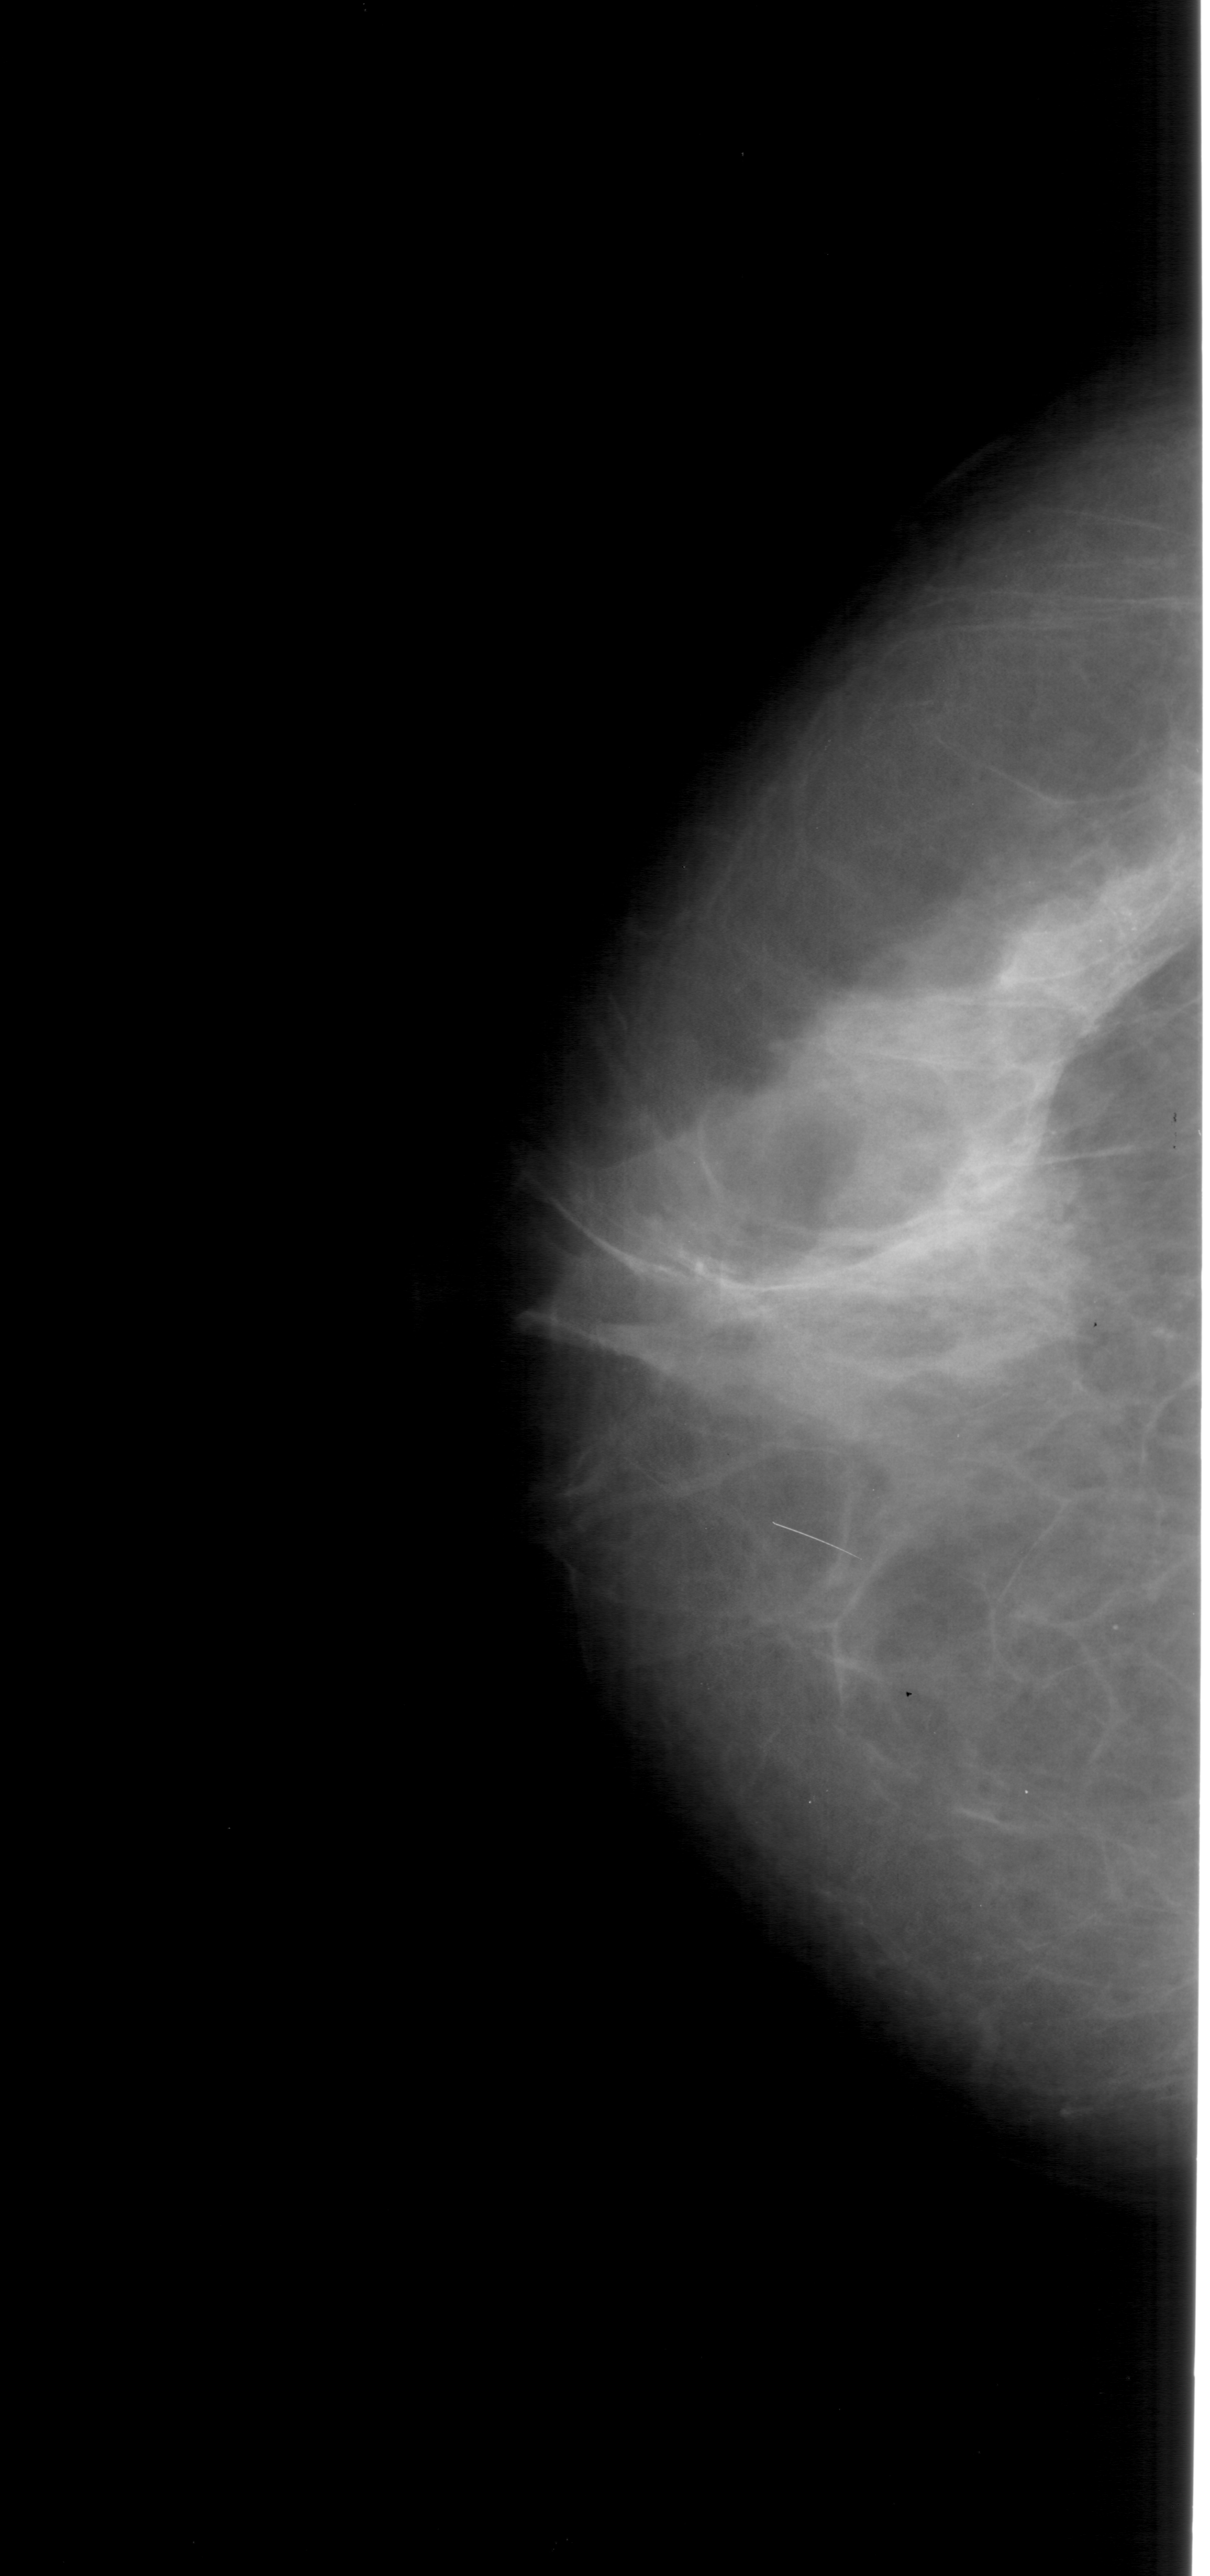
Digitized screen-film mammogram; left breast; CC view; 1210 × 2576 image matrix.
Expert-marked regions of interest on this film, with their recorded descriptors:
- calcifications, morphology pleomorphic, distribution clustered; BI-RADS assessment category 4; pathology (as recorded): benign: bounding box (x1, y1, x2, y2) in pixels: (1087, 897, 1151, 957)